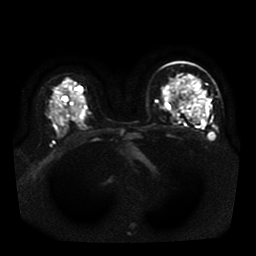
Breast MRI, one axial slice; position 27 of 41 along the scan axis; diffusion-weighted series; image 2 of 4 stored at this slice position (different b-values; order by instance number); 1.5 T; 5 mm slice thickness; 256 × 256 image matrix. Female patient.
Outlined on this slice (manually delineated by an expert):
- tumour on diffusion-weighted imaging: bounding box [x1, y1, x2, y2] px = [200, 99, 204, 112]